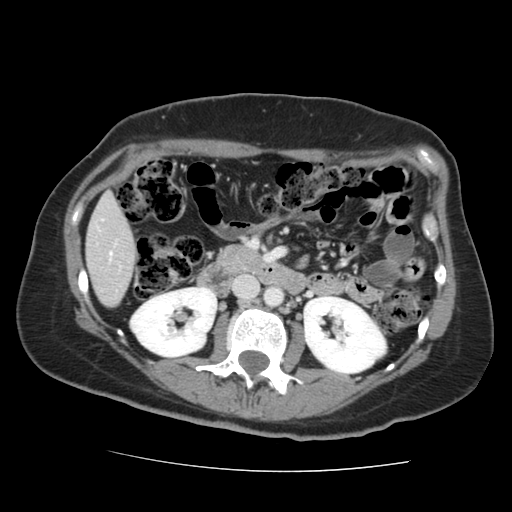
Contrast-enhanced abdominal CT, one axial slice. Slice 55 of 144 in the series (ordered by position). 120 kVp. Intravenous contrast given. Soft-tissue window (W 400 / L 40 HU). 512 × 512 image matrix, field of view 333 × 333 mm. Female patient, age 46 years. From the clinical record (not read from this slice): diagnosis: colorectal cancer liver metastases, imaged before liver resection; multiple liver metastases: no; largest metastasis: 2.8 cm.
Annotated regions visible in this slice (outlined manually by an expert reader):
- liver: bounding box [x1, y1, x2, y2] px = [87, 196, 134, 306]
- planned liver remnant (the part of the liver to remain after resection): [87, 196, 134, 306]
- portal vein (with intrahepatic branches): [109, 253, 112, 256]